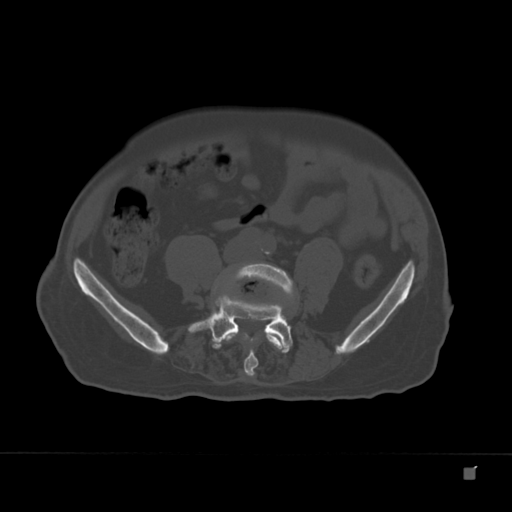
CT including the spine, one axial slice. Position 31 of 332 along the scan axis. 120 kVp. Bone window (W 1800 / L 400 HU). 512 × 512 image matrix, field of view 389 × 389 mm. Patient: male, 72 years. Case-level facts recorded for this patient, not image findings: primary cancer: skeletal.
Annotated regions visible in this slice (semi-automatically segmented with operator editing):
- L4 vertebra: box from (x=227, y=263) to (x=294, y=376) px
- L5 vertebra: (x=192, y=294)–(x=293, y=351)